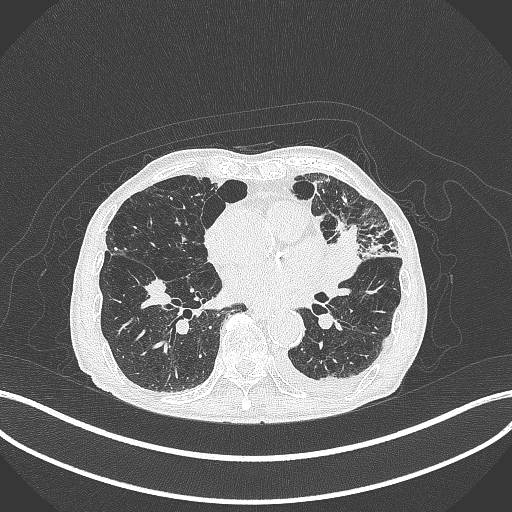
Chest CT, one axial slice. Slice 165 of 385 in the series (ordered by position). 120 kVp. Lung window (W 1500 / L -600 HU). 1 mm slice thickness. 512 × 512 image matrix. Patient: male, 90 years or older. Case-level facts recorded for this patient, not image findings: clinical TNM (as recorded): T2b N1 M0.
Annotated regions visible in this slice (bounding box drawn by a radiologist):
- lung tumour (recorded histology: squamous cell carcinoma): bounding box (x1, y1, x2, y2) in pixels: (330, 219, 368, 281)